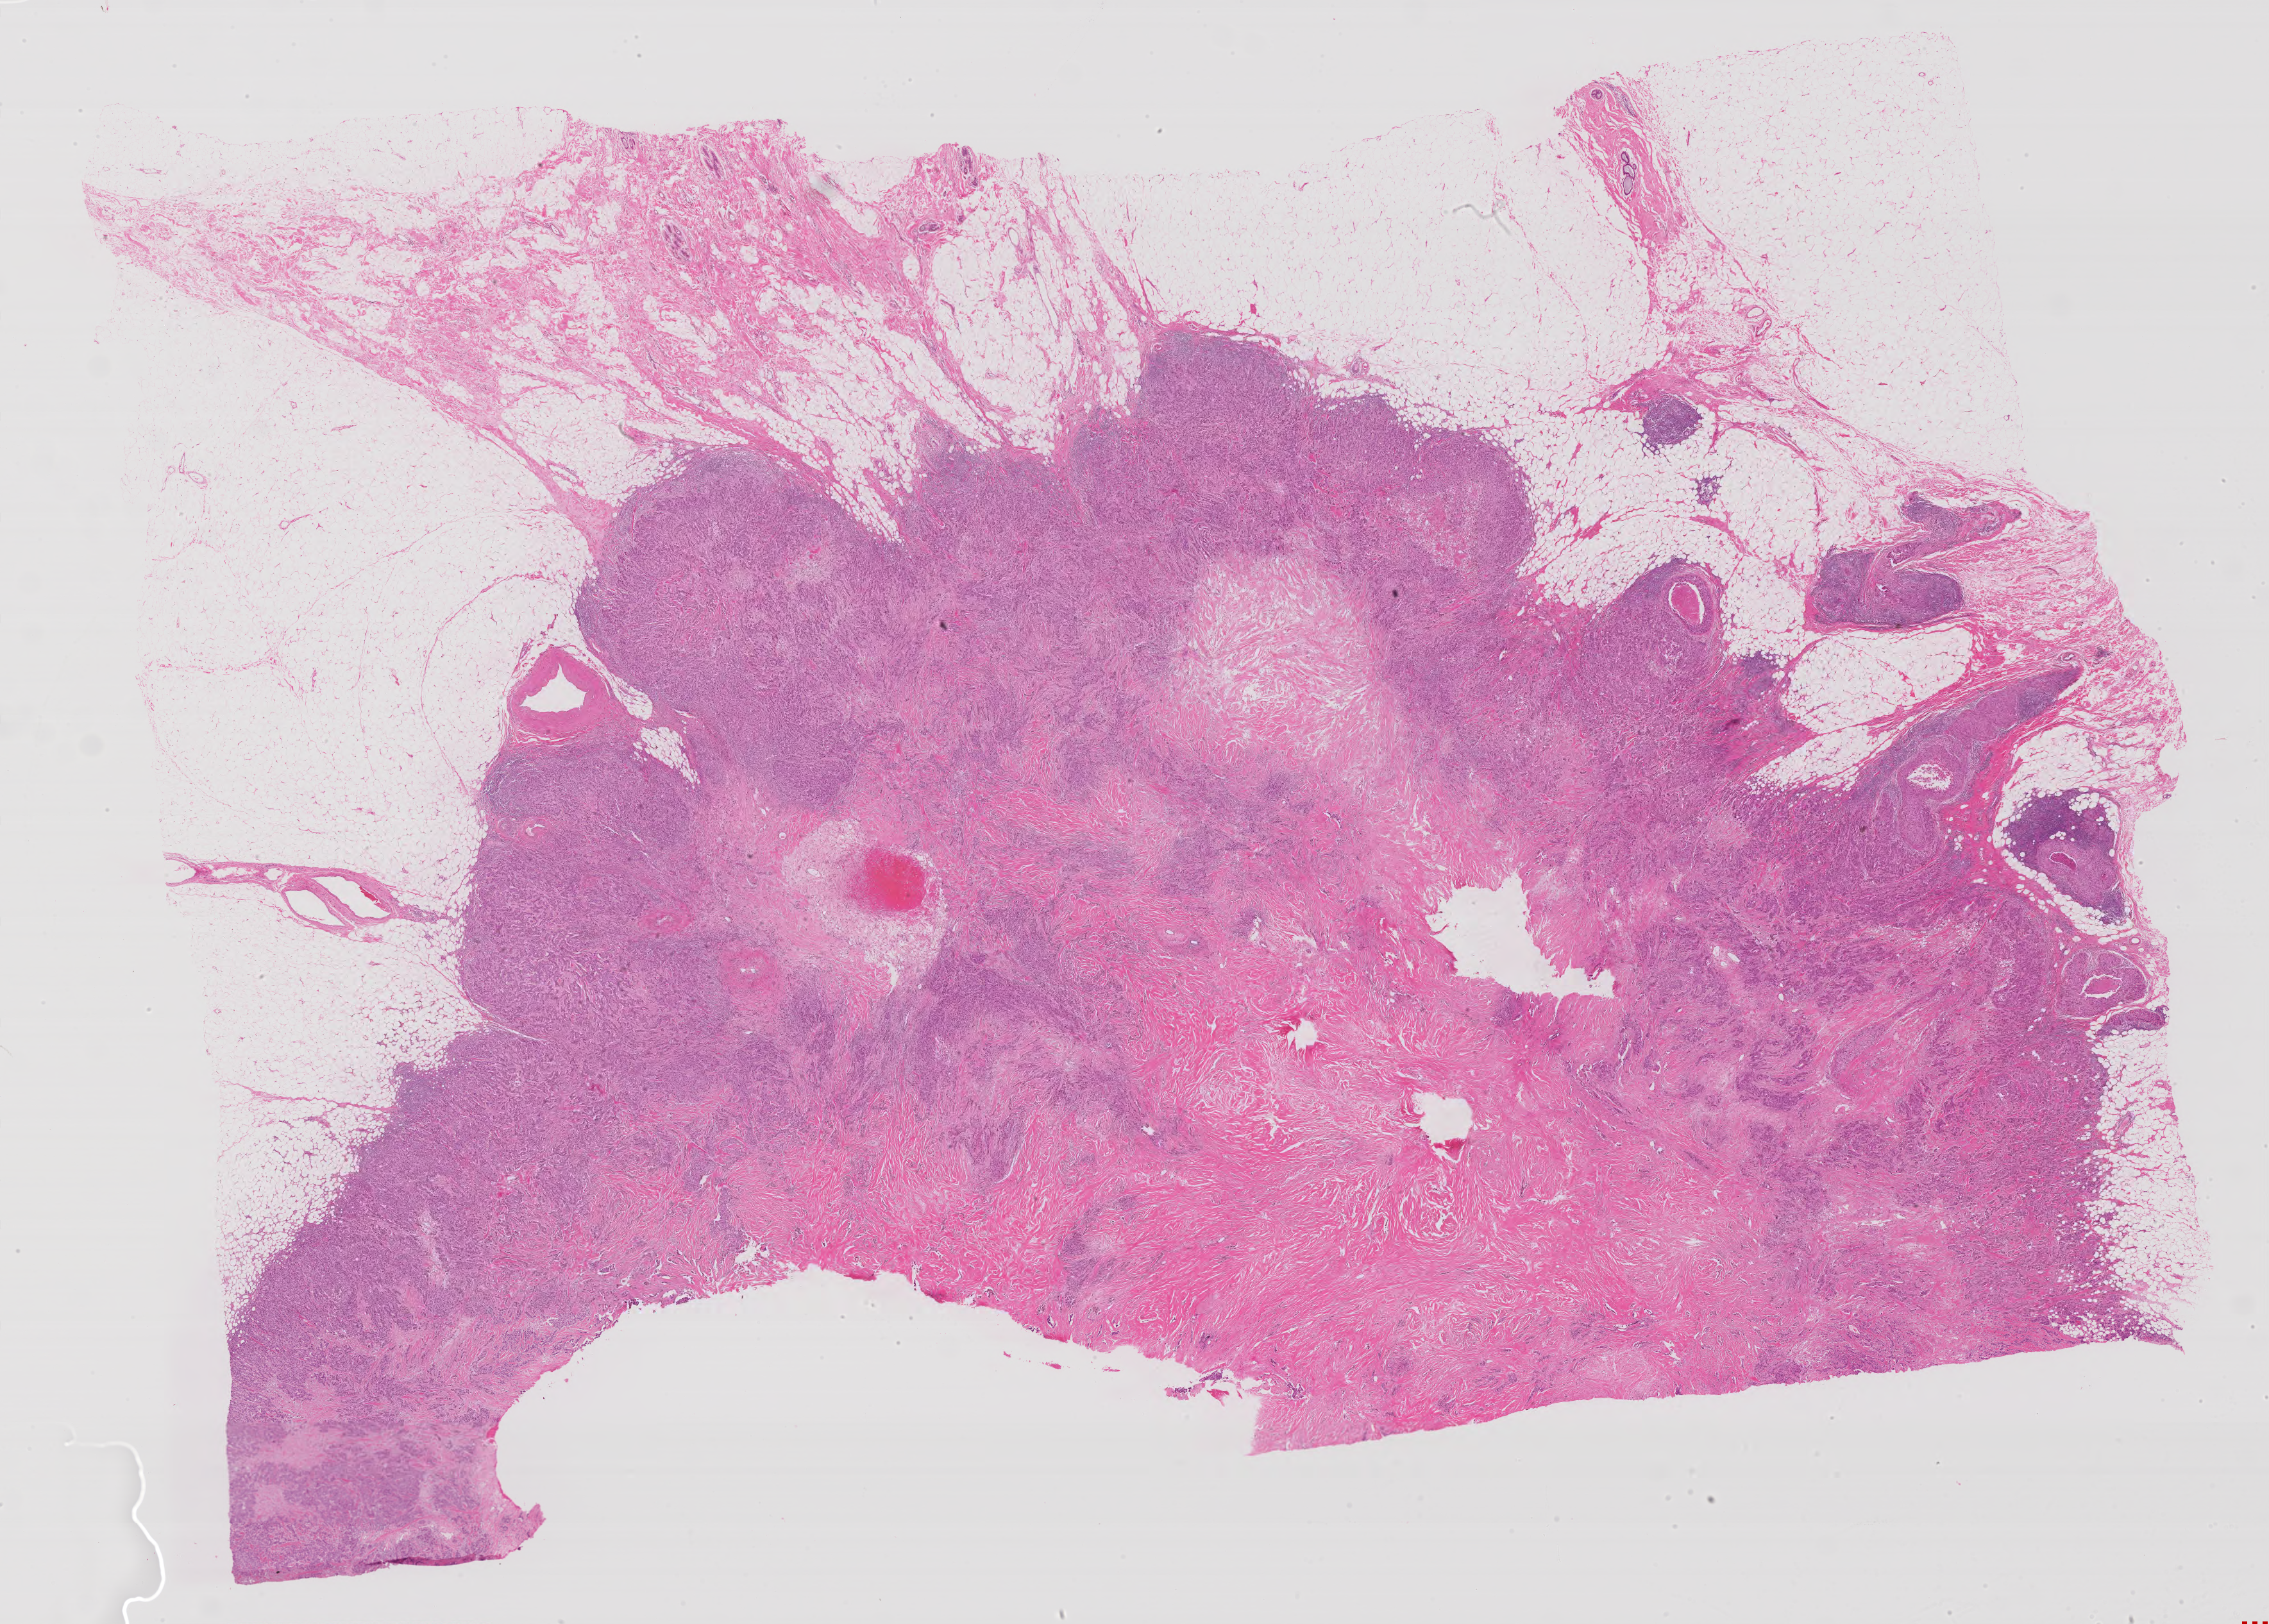
Whole-slide histology image, H&E-stained, whole scanned area (about 28.3 x 20.3 mm) shown as a low-resolution overview, formalin-fixed paraffin-embedded (FFPE) diagnostic section, breast, primary tumour sample. Female, age 50 years at initial diagnosis.
* lymph nodes positive (case pathology): 1 of 15 examined
* laterality: right
* diagnosis: Infiltrating duct carcinoma, NOS
* AJCC pathologic stage: IIB (6th edition)